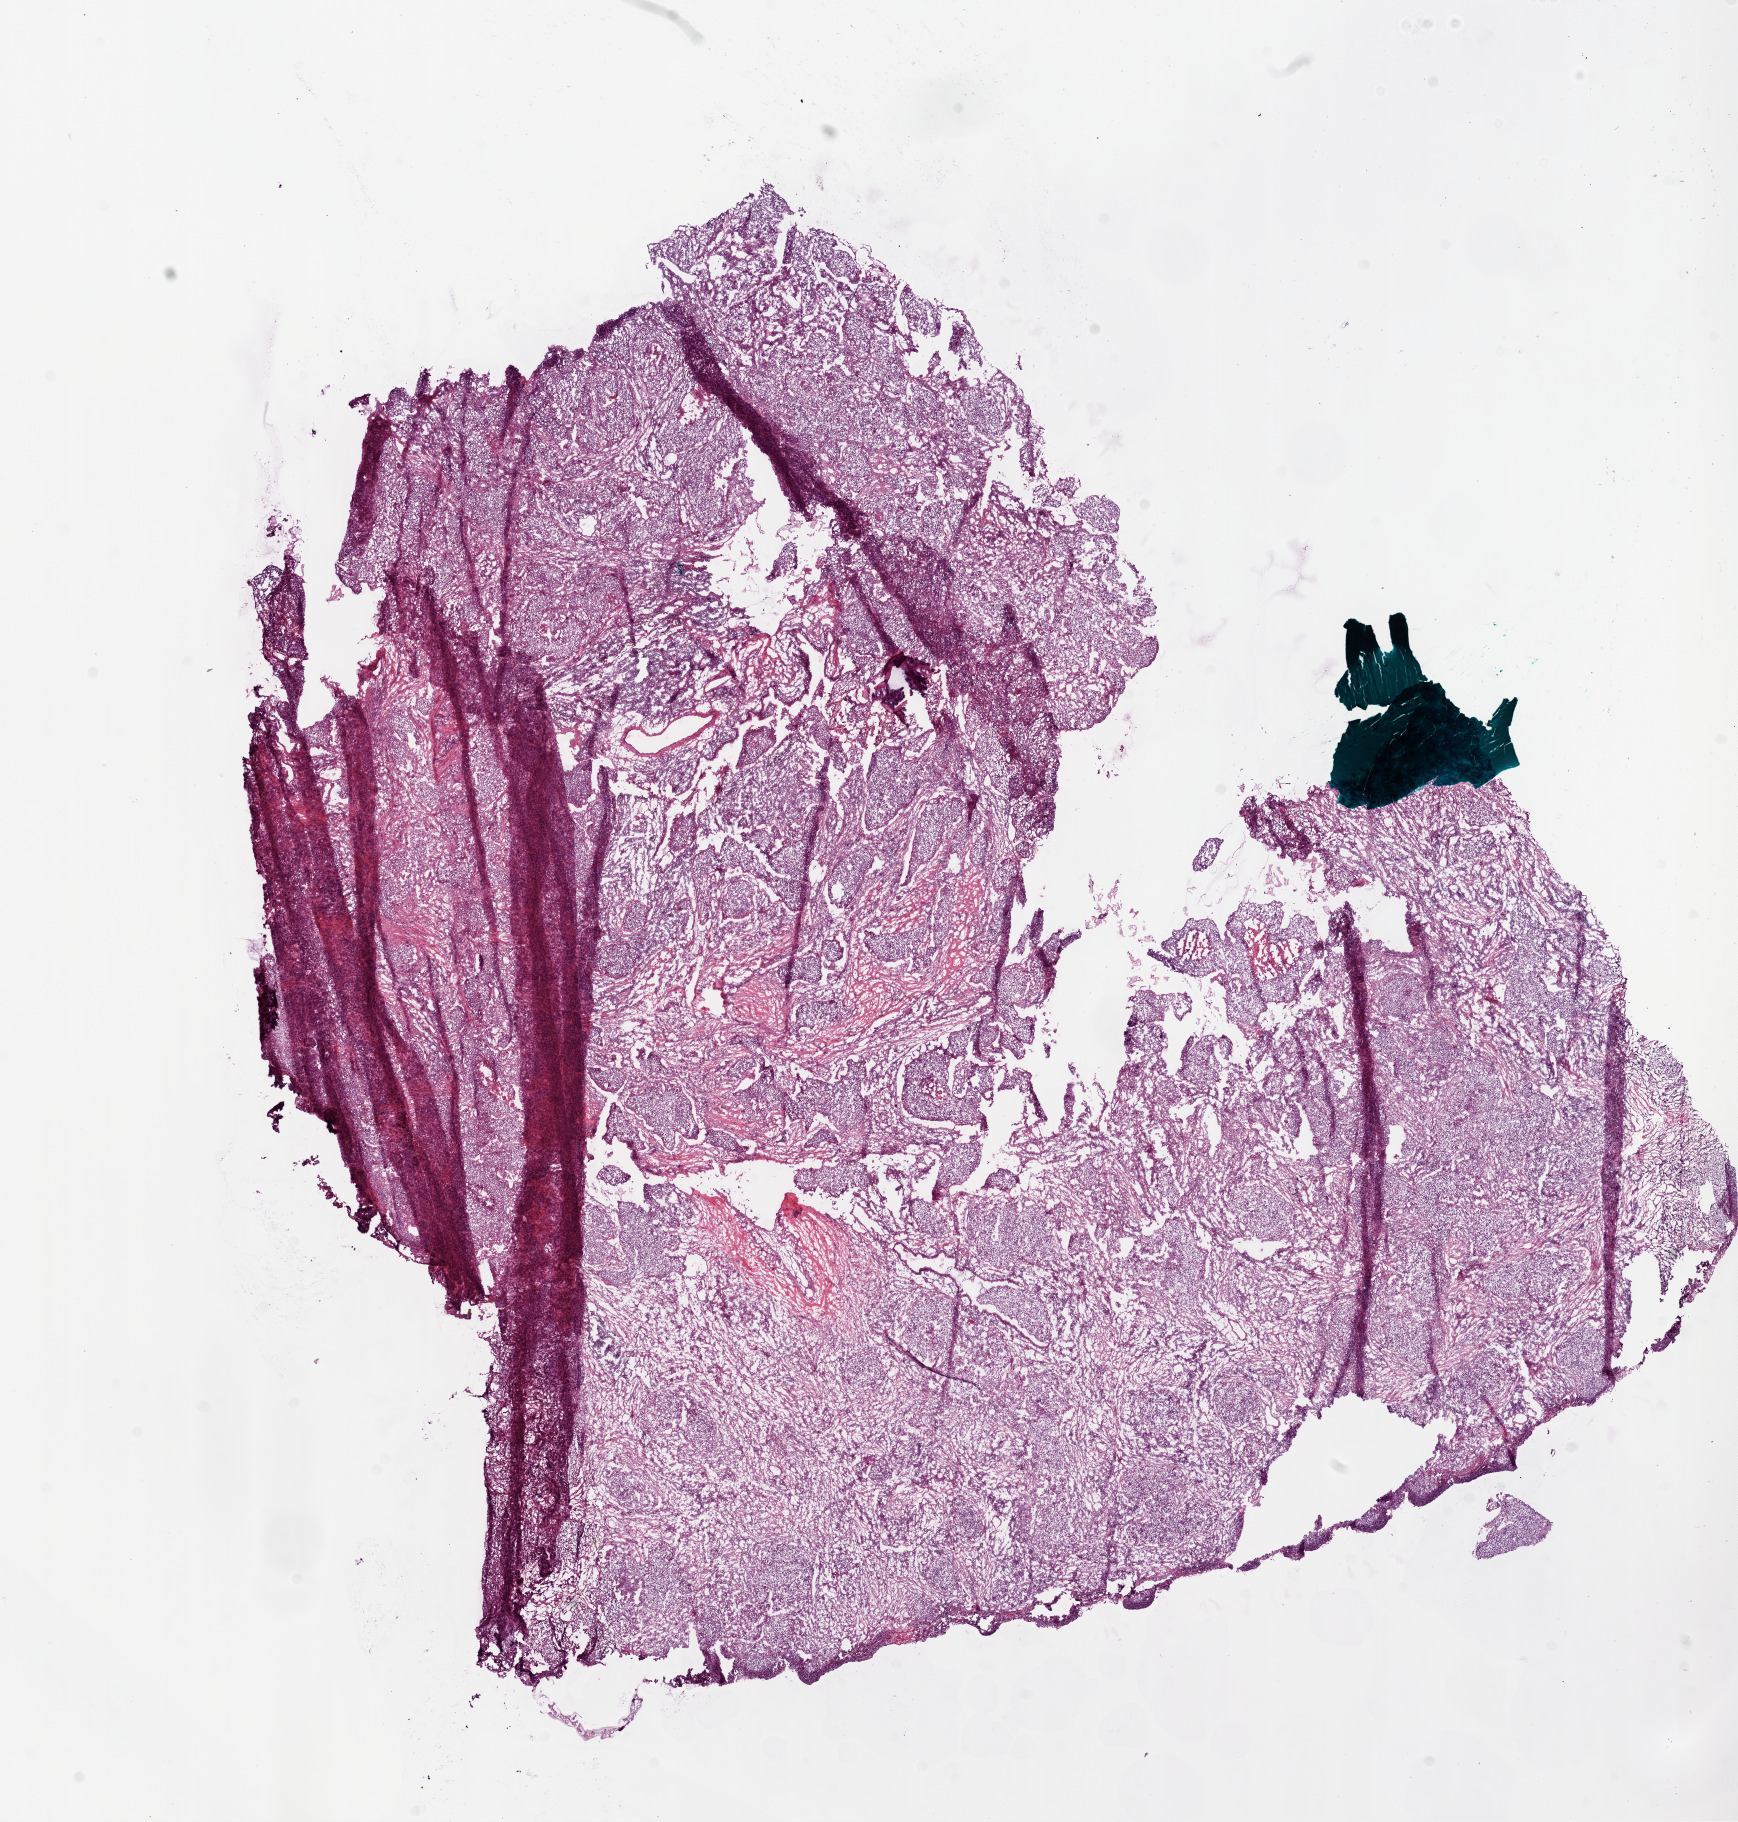
H&E-stained whole-slide image, a low-resolution overview of the entire scanned area, about 14.0 x 14.7 mm (acquisition: 20x scan), frozen section from the bottom of the tissue portion, primary tumour sample from the lung. Male patient; age at initial diagnosis 61 years. Composition of this section per pathologist review: tumour nuclei 90%, necrosis 2%.
AJCC pathologic stage: IB. Laterality: left. Pathologic diagnosis: Squamous cell carcinoma, NOS.